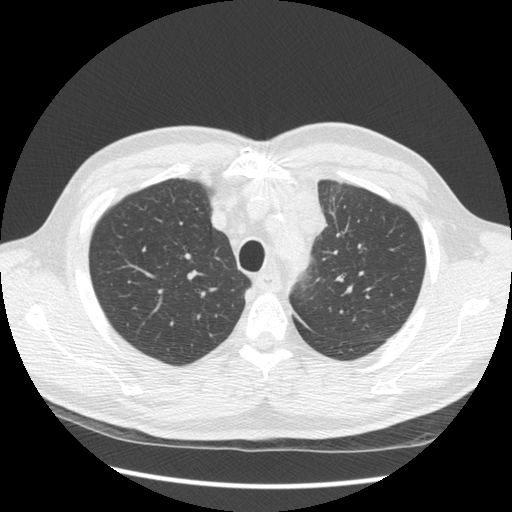
Low-dose screening chest CT, one axial slice; position 109 of 136 along the scan axis; 120 kVp; lung window (W 1500 / L -600 HU); 2.5 mm slice thickness; 512 × 512 image matrix, field of view 360 × 360 mm.
Annotated regions visible in this slice (manually delineated by an expert):
- lesion 1 (tumor, upper lobe of left lung): box from (x=294, y=182) to (x=324, y=241) px